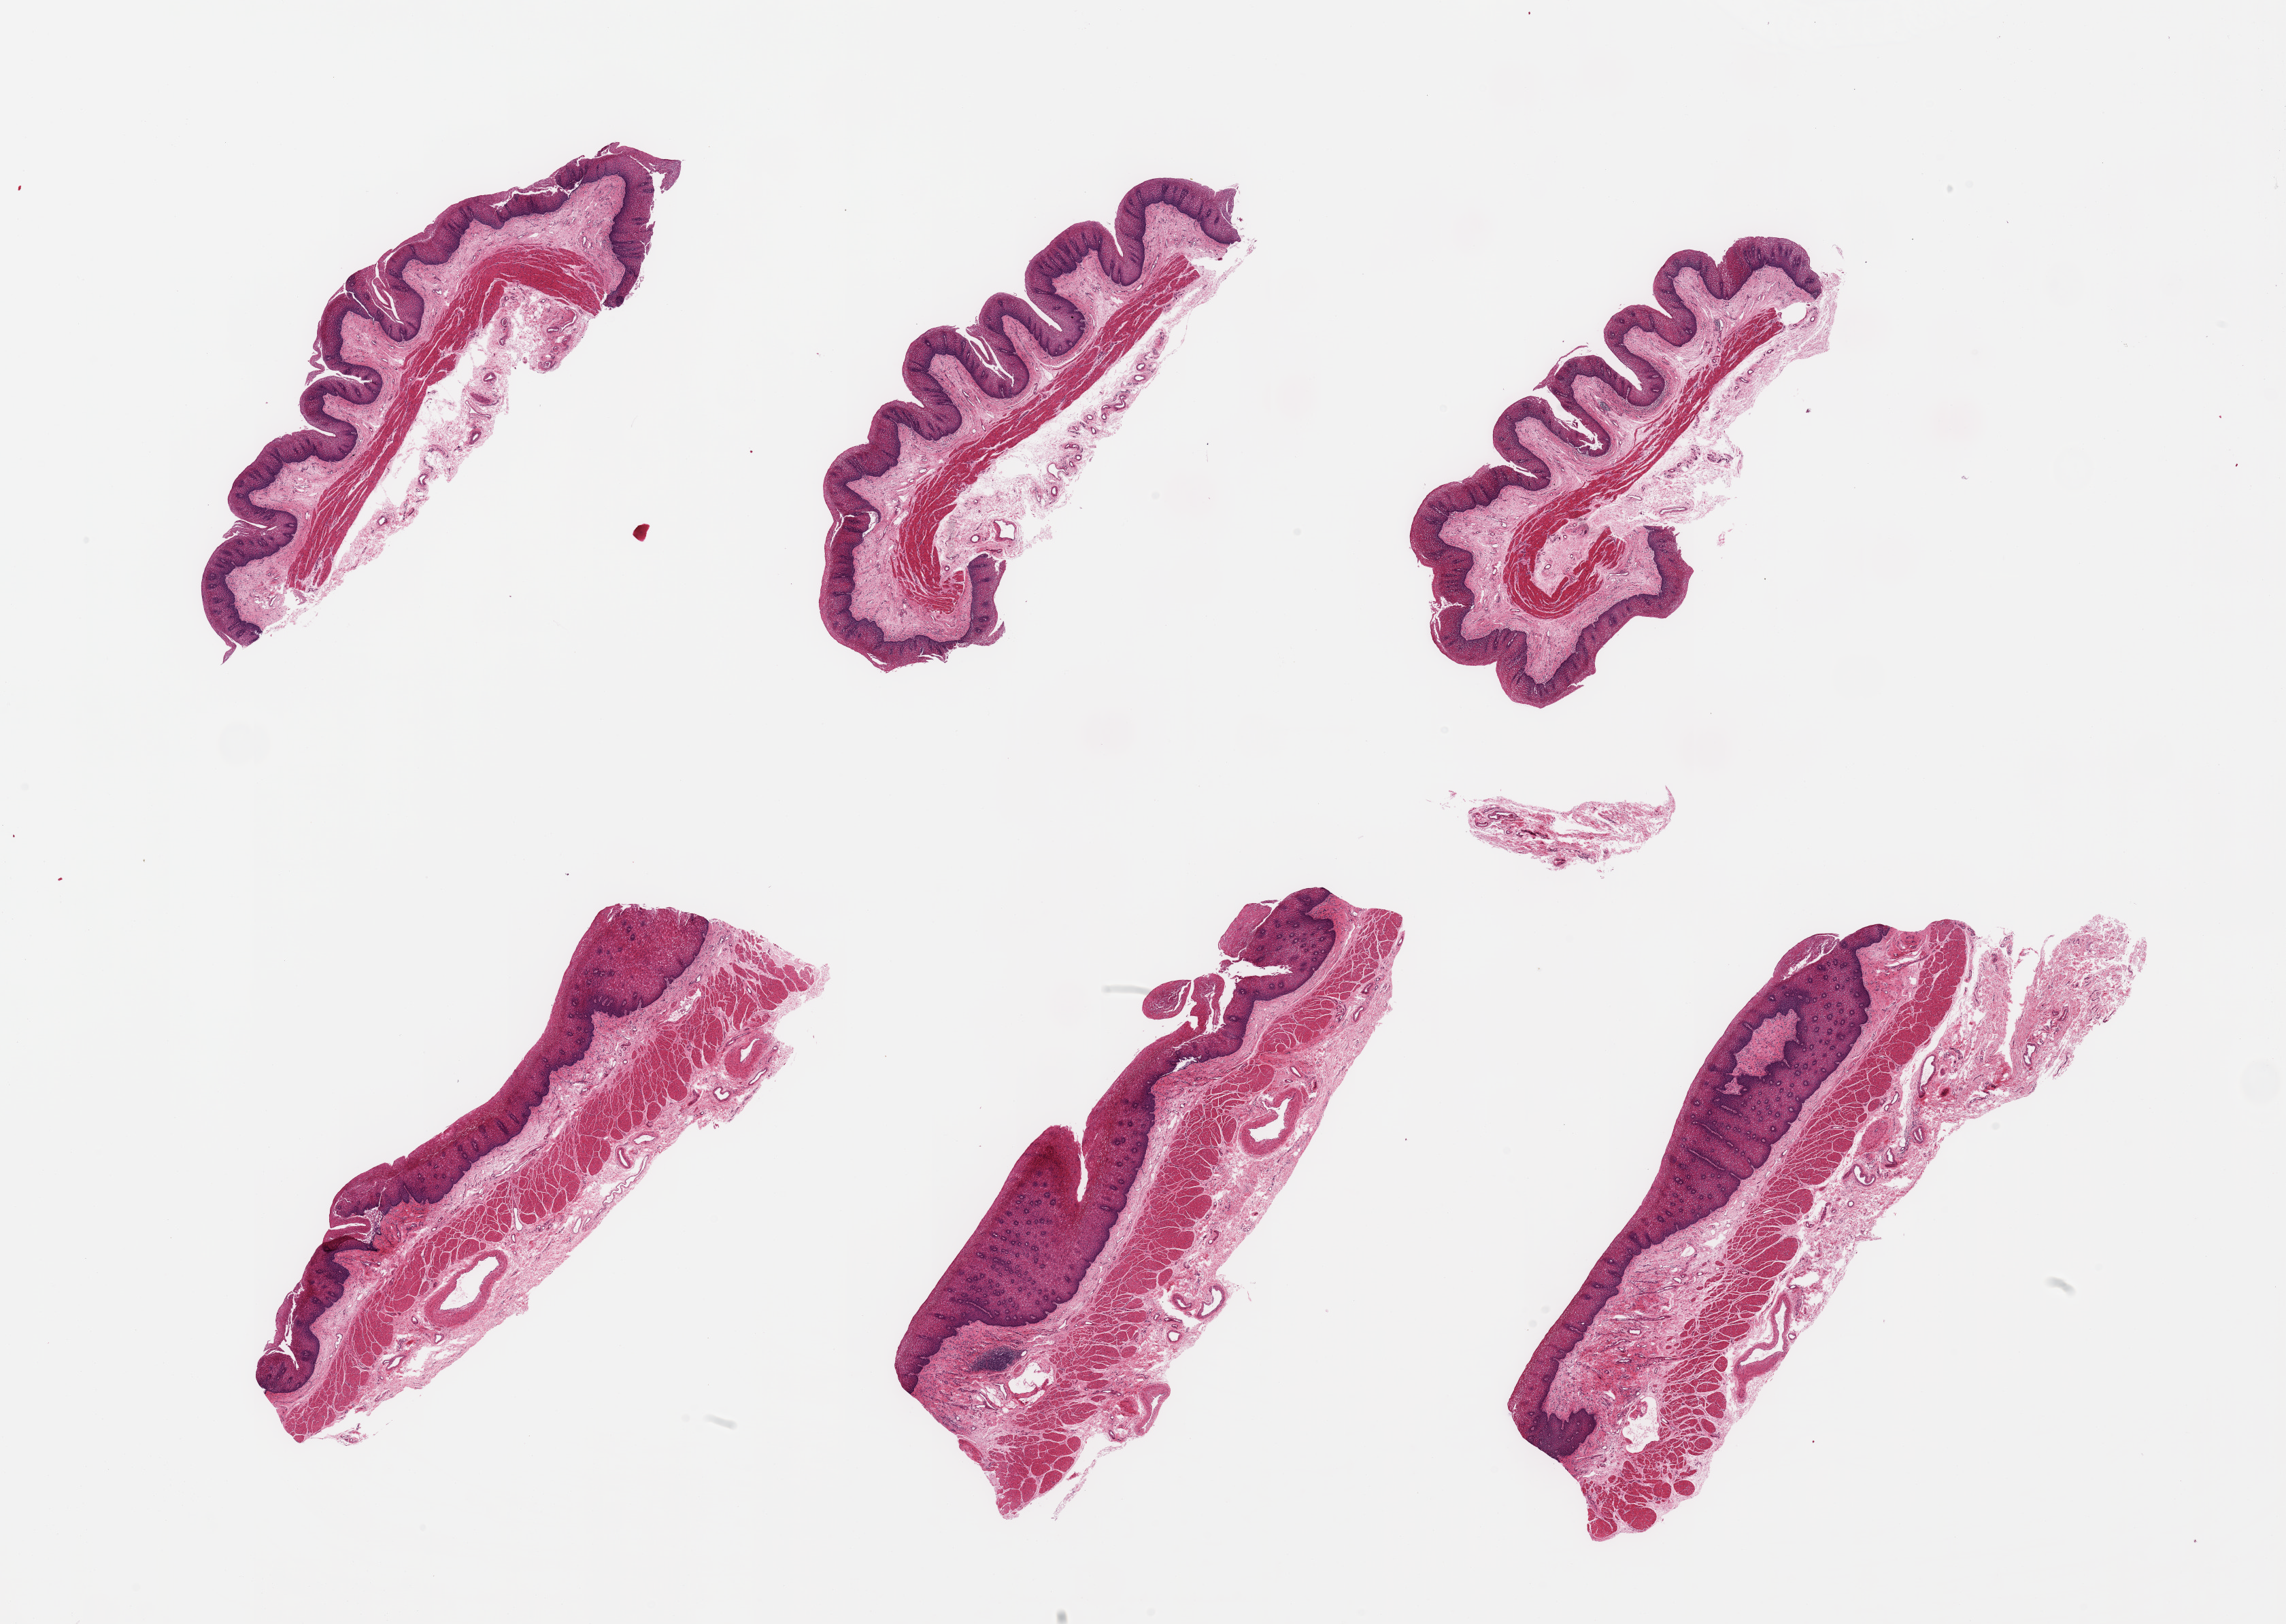
Digitized haematoxylin and eosin-stained section, shown as a low-resolution overview of the whole scanned area (about 26.6 x 18.9 mm); PAXgene-fixed, paraffin-embedded tissue; target tissue: esophageal mucous membrane; tissue donor sample. Male donor.
Pathologist's review note for this sample: 6 pieces; well dissected; prominent muscularis mucosae.